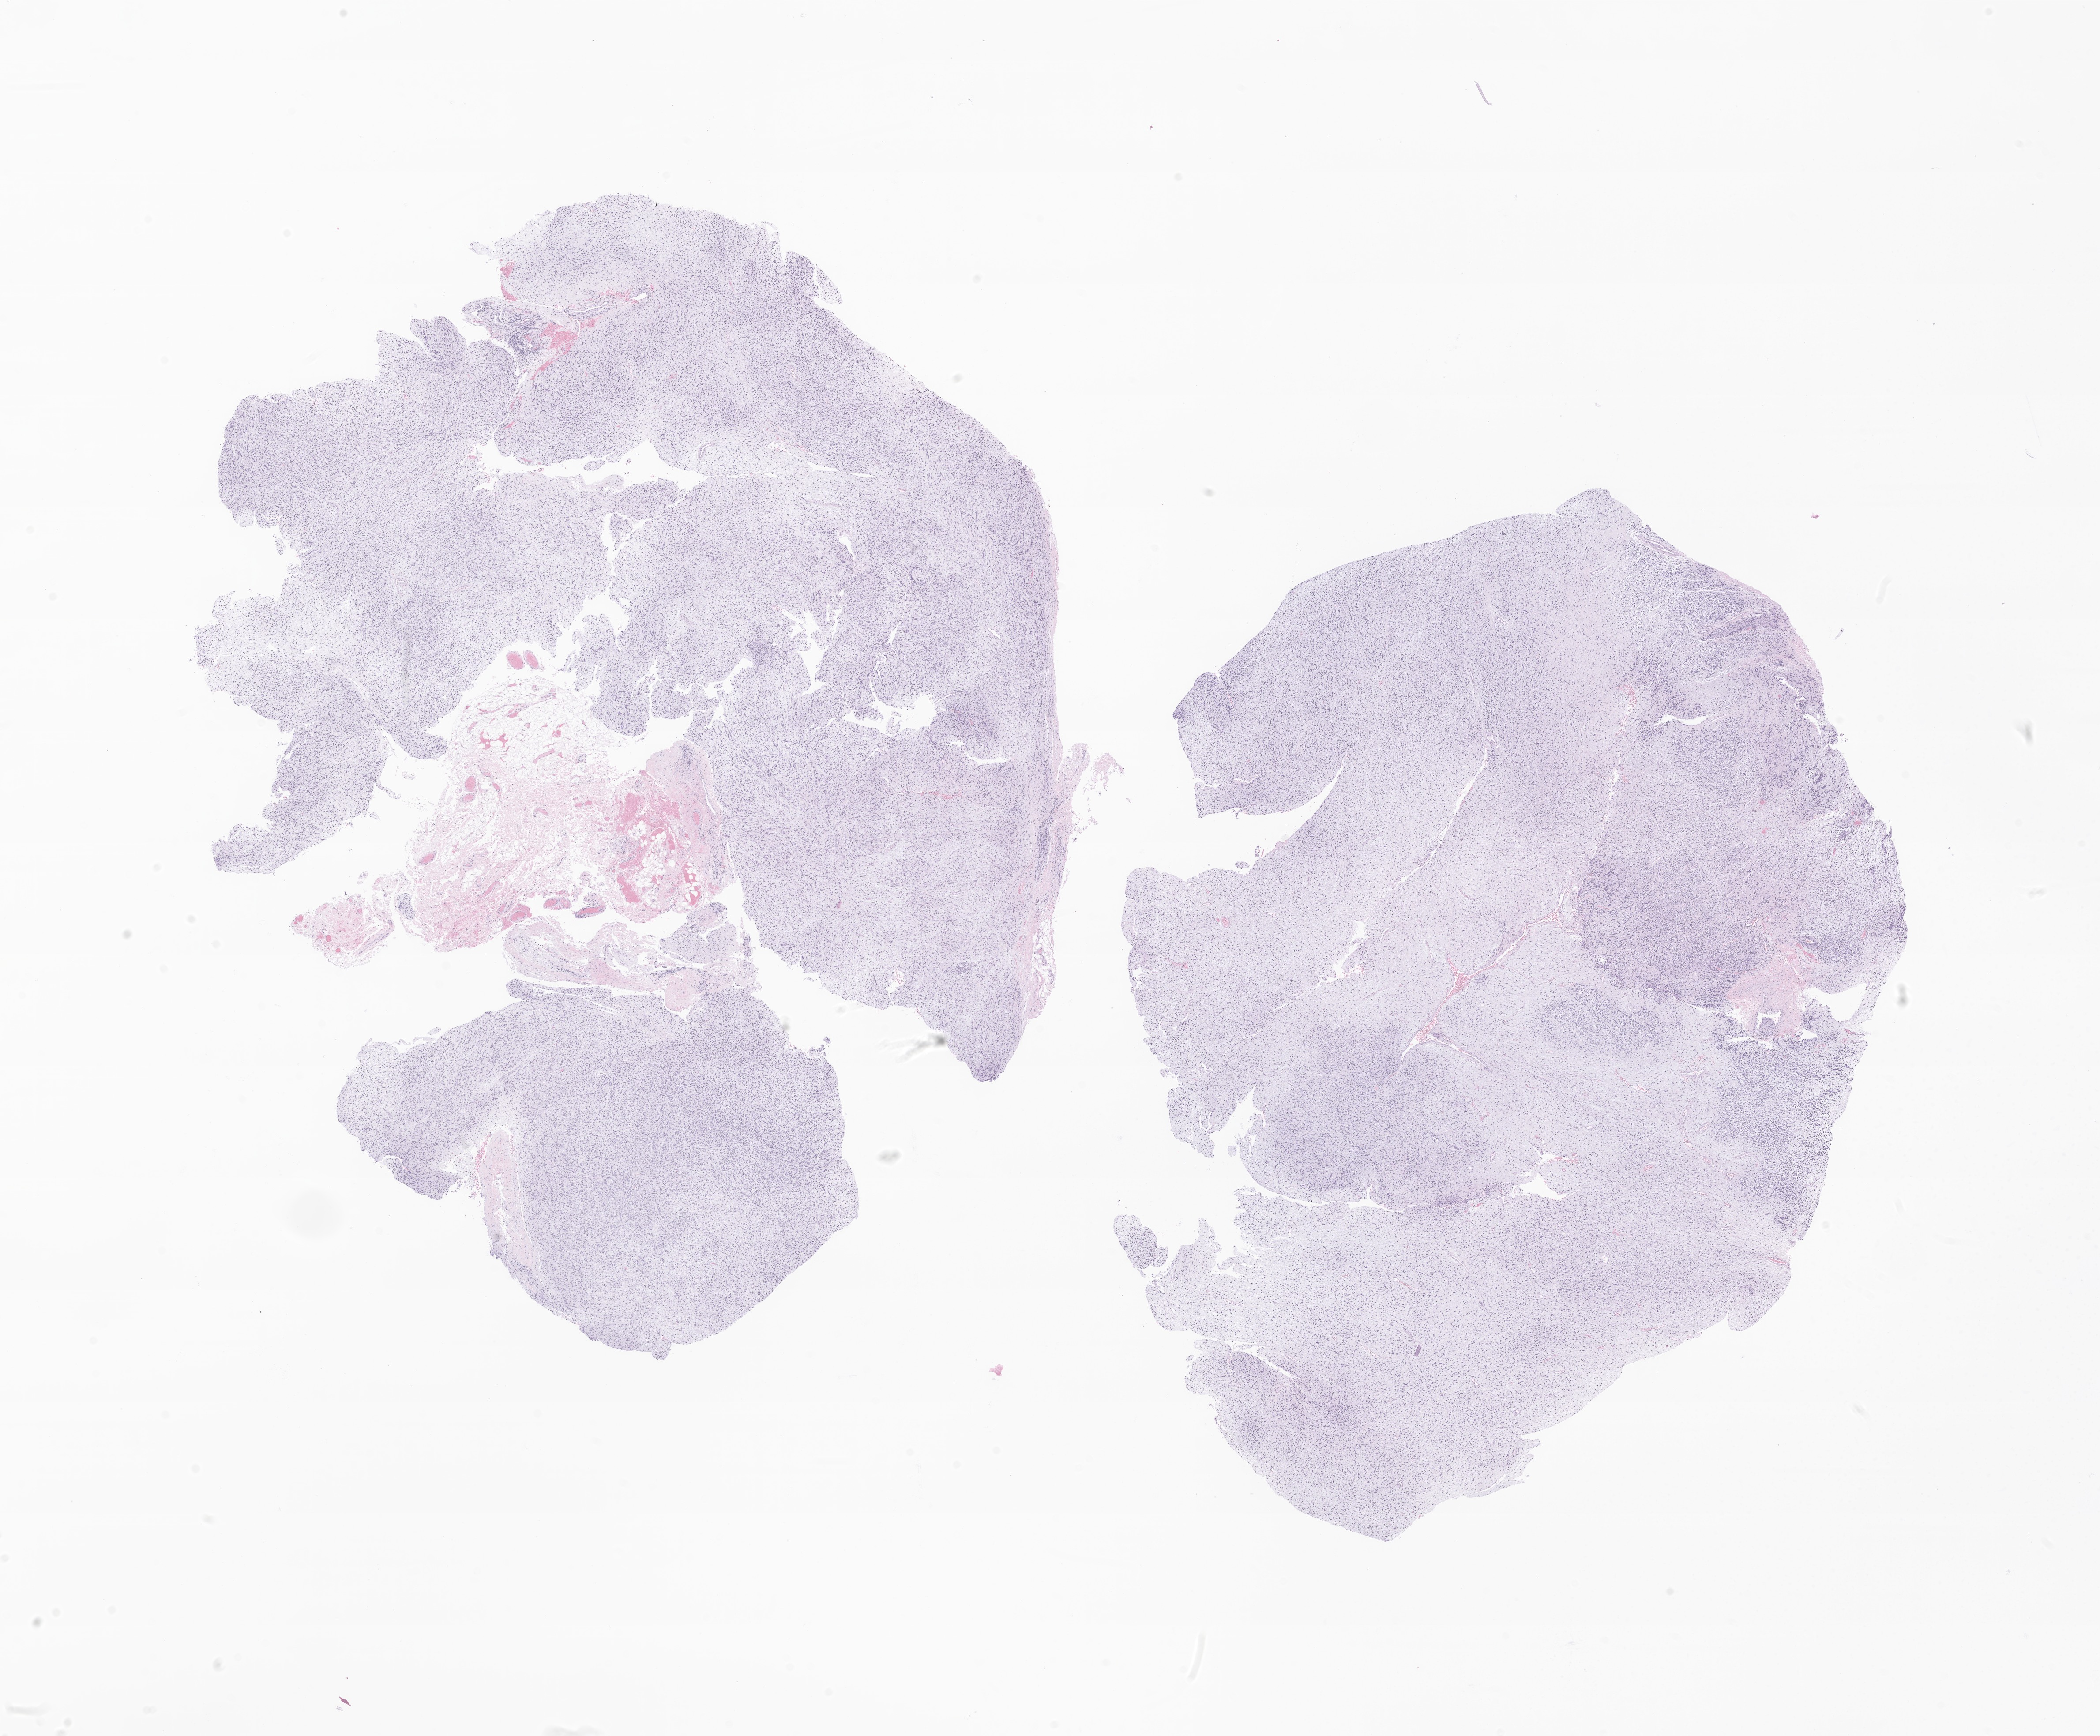
Digitized hematoxylin and eosin (H&E)-stained section of tumor tissue from the orbit — whole scanned area (about 20.1 x 16.6 mm) shown as a low-resolution overview; formalin-fixed paraffin-embedded section. Patient: male, age 155 months (12 years 11 months).
- diagnosis: Embryonal rhabdomyosarcoma, NOS